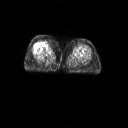
FDG PET of an extremity soft-tissue mass (from a PET/CT study), one axial slice. Slice 15 of 267 in the series (ordered by position). 3.27 mm slice thickness. 128 × 128 image matrix, field of view 700 × 700 mm. Patient: female, 56 years. Case-level facts recorded for this patient, not image findings: histological type: malignant solitary fibrous tumor; grade: intermediate; site of the primary tumour: right thigh.
Annotated regions visible in this slice (expert contour drawn on MRI and transferred to this co-registered scan by the dataset authors):
- gross tumour volume including surrounding oedema: bounding box [x1, y1, x2, y2] px = [41, 41, 51, 48]